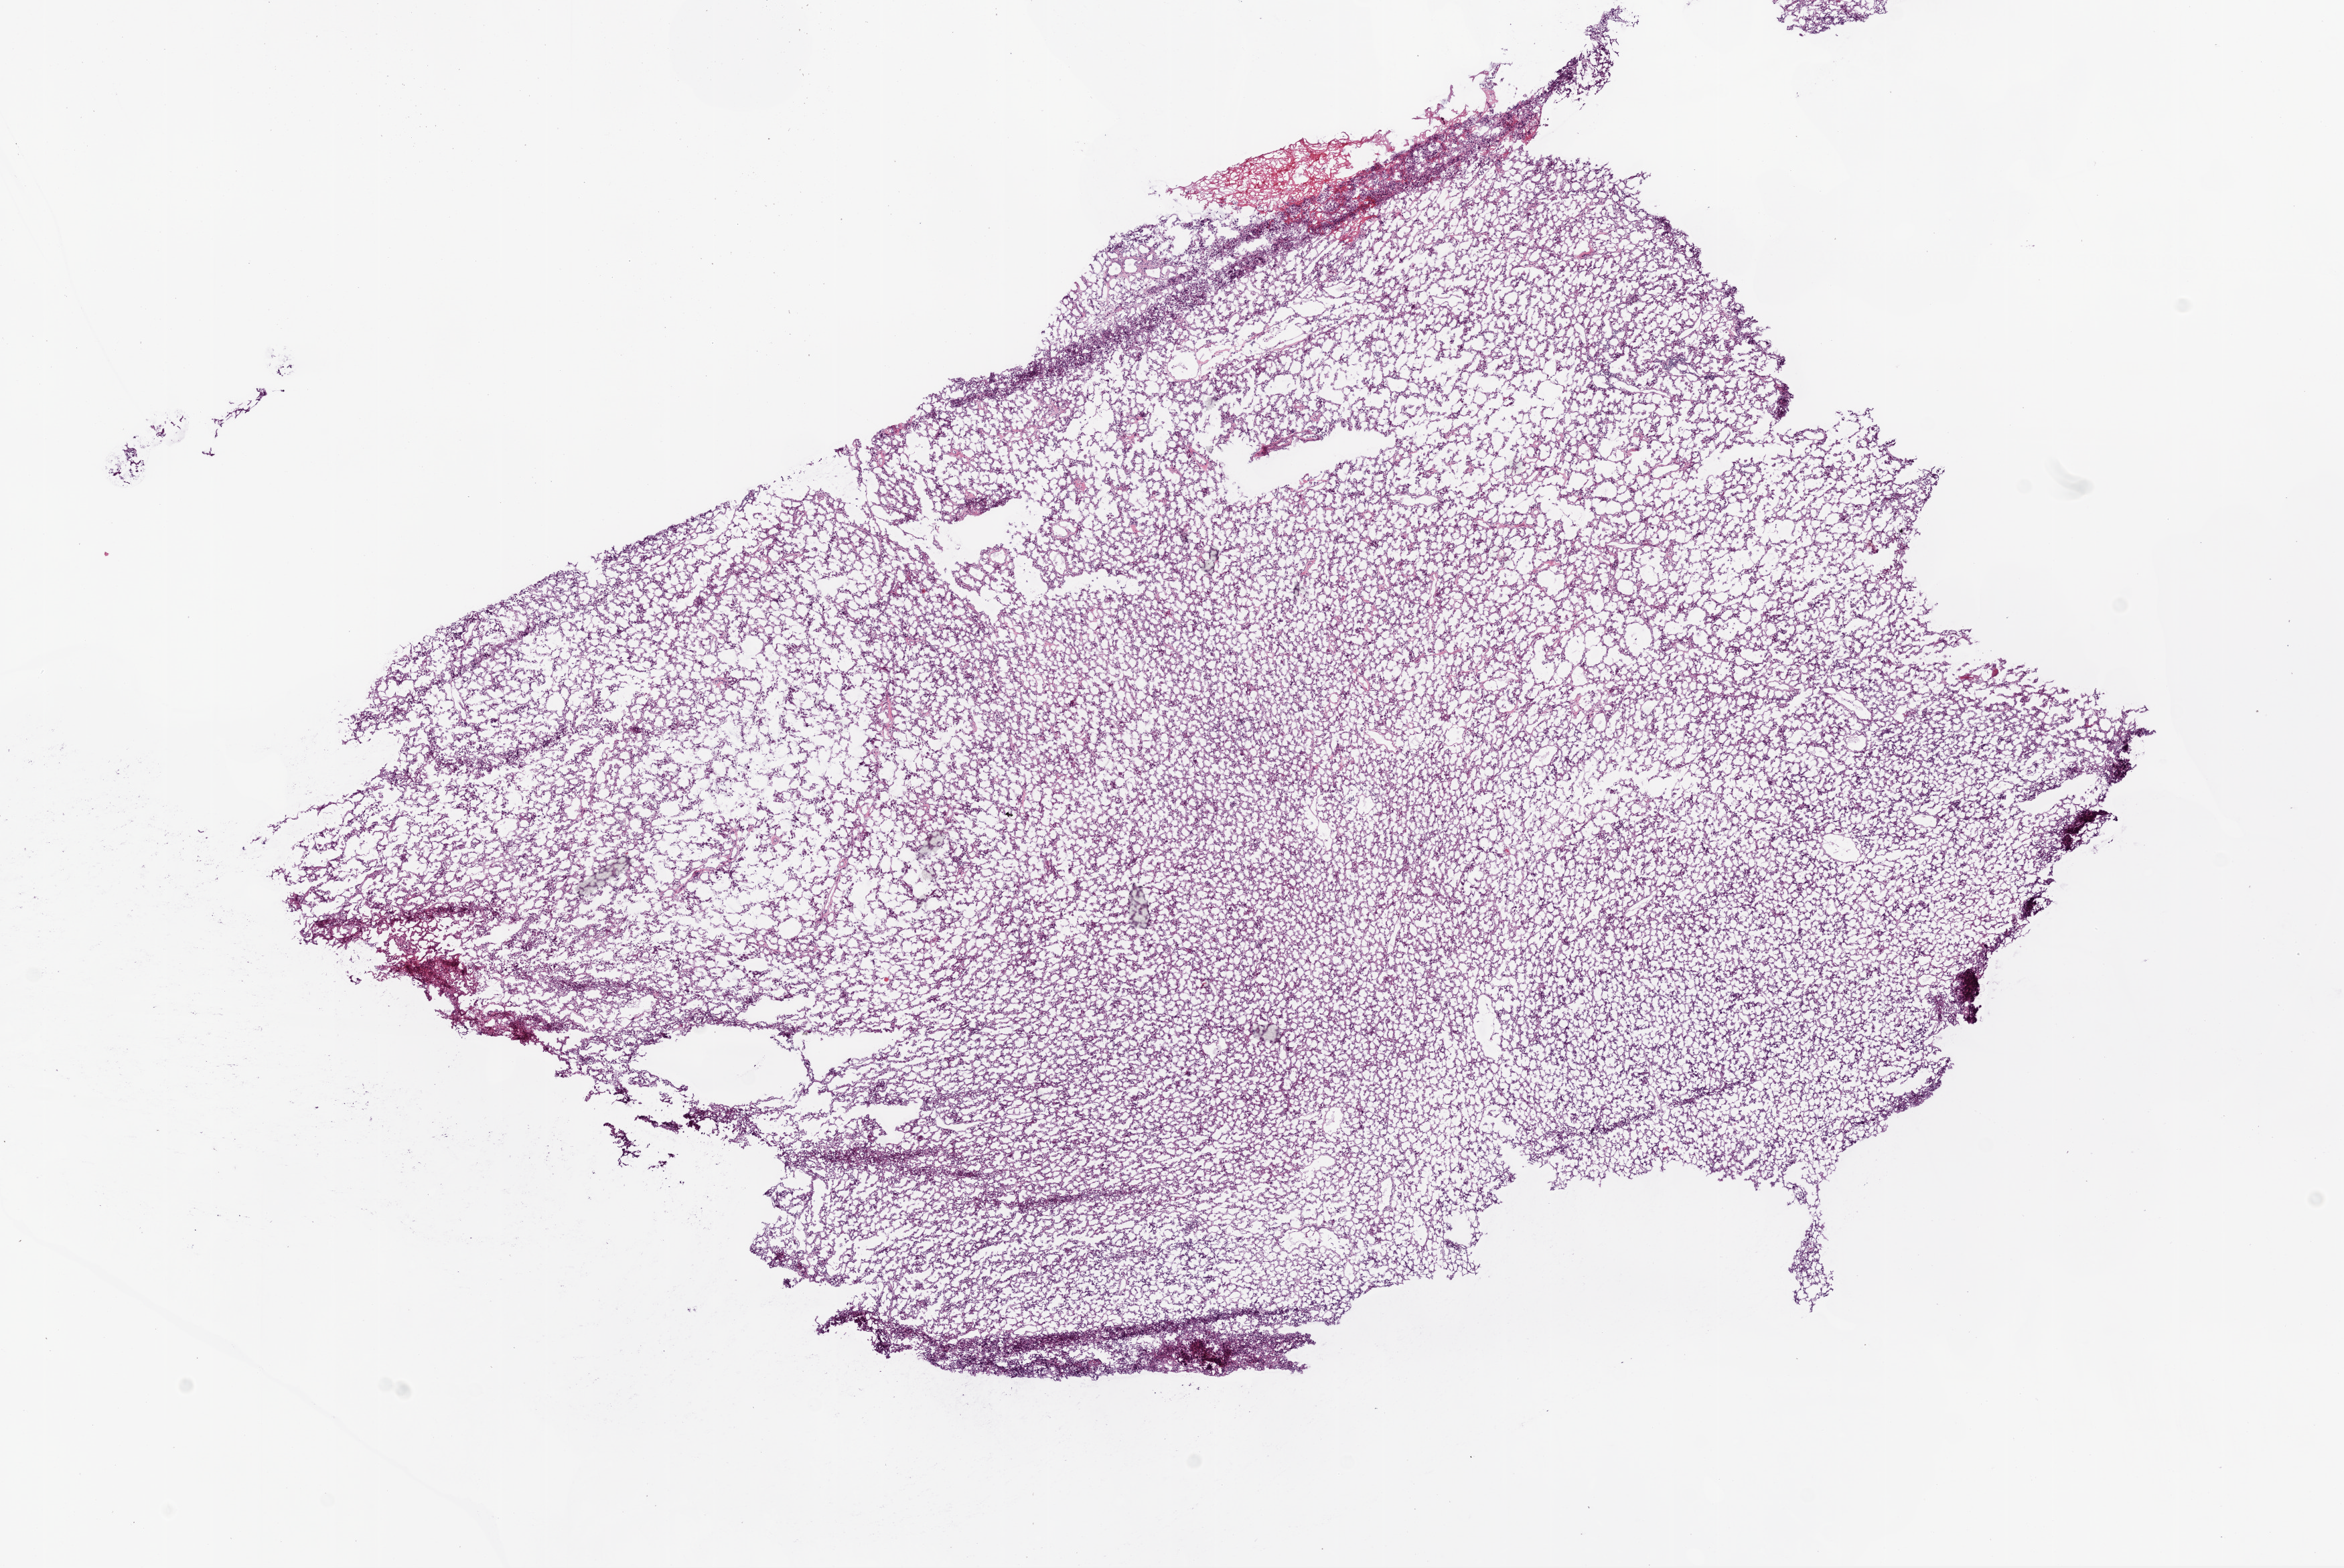
Digitized H&E tissue section (whole slide), low-resolution overview of the scanned area, about 14.0 x 9.4 mm, frozen section from the bottom of the tissue portion, primary tumour sample from the brain. Patient: female, age at initial diagnosis 59 years. Slide review estimates, as recorded: tumour cells 95%, tumour nuclei 95%, normal cells 0%, stromal cells 0%, necrosis 5%.
- pathologic diagnosis: Glioblastoma